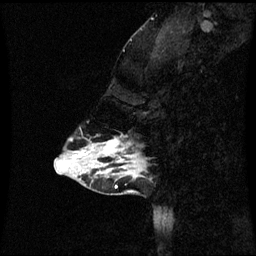
Breast MRI (dynamic contrast-enhanced), one sagittal slice. Slice 17 of 60 in the series (ordered by position). Dynamic contrast-enhanced series, image 2 of 3 at this slice position (ordered by acquisition). 1.5 T. TE 4.2 ms, TR 8.9 ms. 256 × 256 image matrix, field of view 220 × 220 mm. Patient: female, 43 years. From the clinical record (not read from this slice): setting: breast cancer imaged before/during neoadjuvant chemotherapy; receptor status: HR-positive, HER2-negative.
Structures marked on this image (semi-automatically segmented with operator editing):
- analysis volume of interest (the breast-tissue region the enhancement analysis was run in; not a lesion): bounding box [x1, y1, x2, y2] px = [84, 140, 144, 171]
- tumour enhancement mask (voxels above the 70 % enhancement threshold inside the analysis volume of interest): [104, 140, 136, 163]